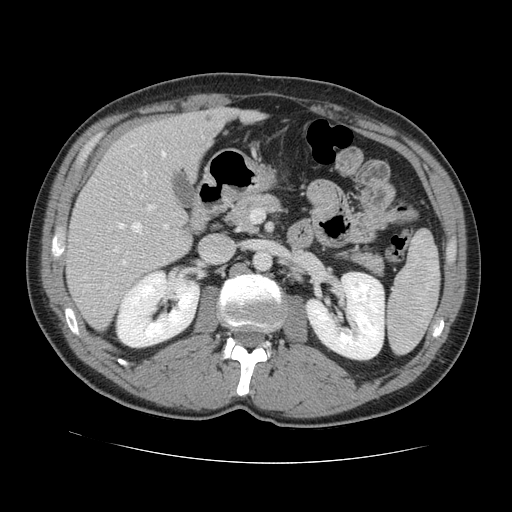
Contrast-enhanced abdominal CT, one axial slice; slice 67 of 131 in the series (ordered by position); 120 kVp; intravenous contrast given; soft-tissue window (W 400 / L 40 HU); 2.5 mm slice thickness; 512 × 512 image matrix, field of view 380 × 380 mm. Male patient, age 40 years. Case-level facts recorded for this patient, not image findings: diagnosis: colorectal cancer liver metastases, imaged before liver resection; multiple liver metastases: yes; largest metastasis: 2.9 cm; disease in both lobes: yes.
Annotated regions visible in this slice (expert manual segmentation):
- hepatic veins: bounding box (x1, y1, x2, y2) in pixels: (114, 144, 167, 251)
- liver: (67, 109, 258, 330)
- planned liver remnant (the part of the liver to remain after resection): (109, 109, 256, 186)
- portal vein (with intrahepatic branches): (122, 170, 168, 265)
- liver metastasis: (207, 117, 212, 121)